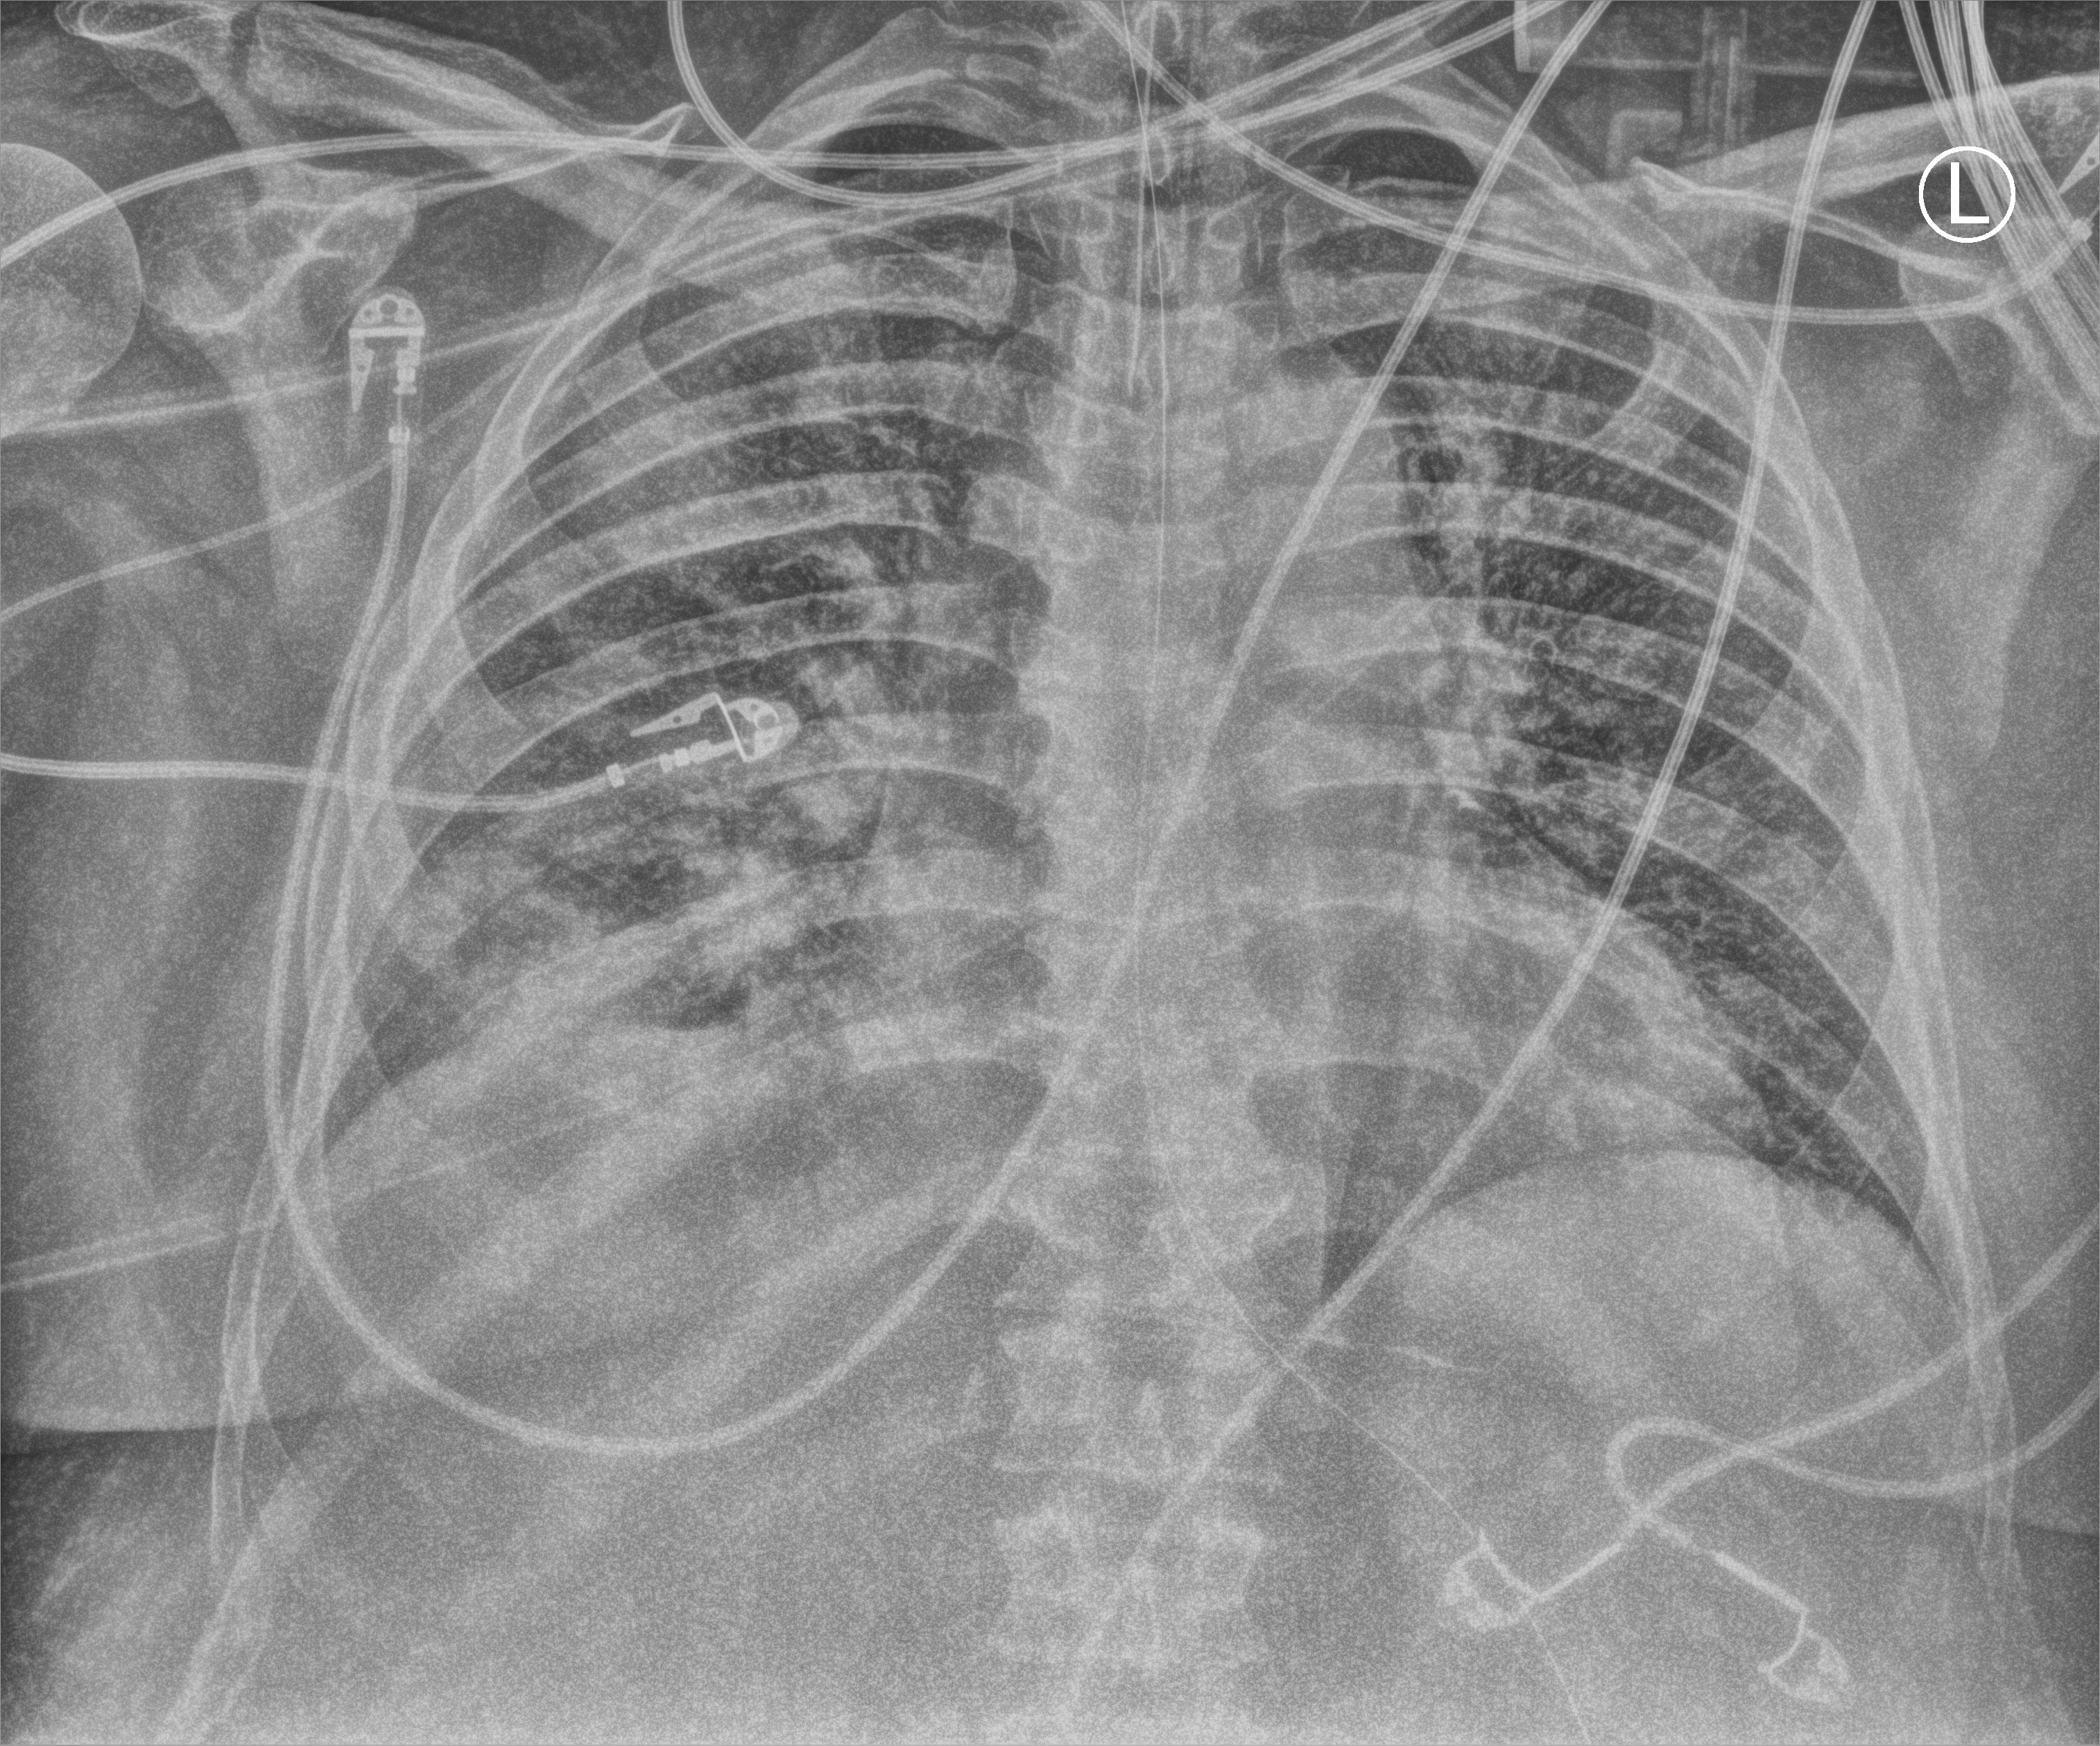
Portable chest radiograph; anteroposterior (AP) projection. Patient hospitalised with COVID-19; male, aged 18–59 years.
Hospital-stay facts (about this admission, not read from this image; timing relative to this image not recorded): admitted to intensive care during this hospital stay: yes.